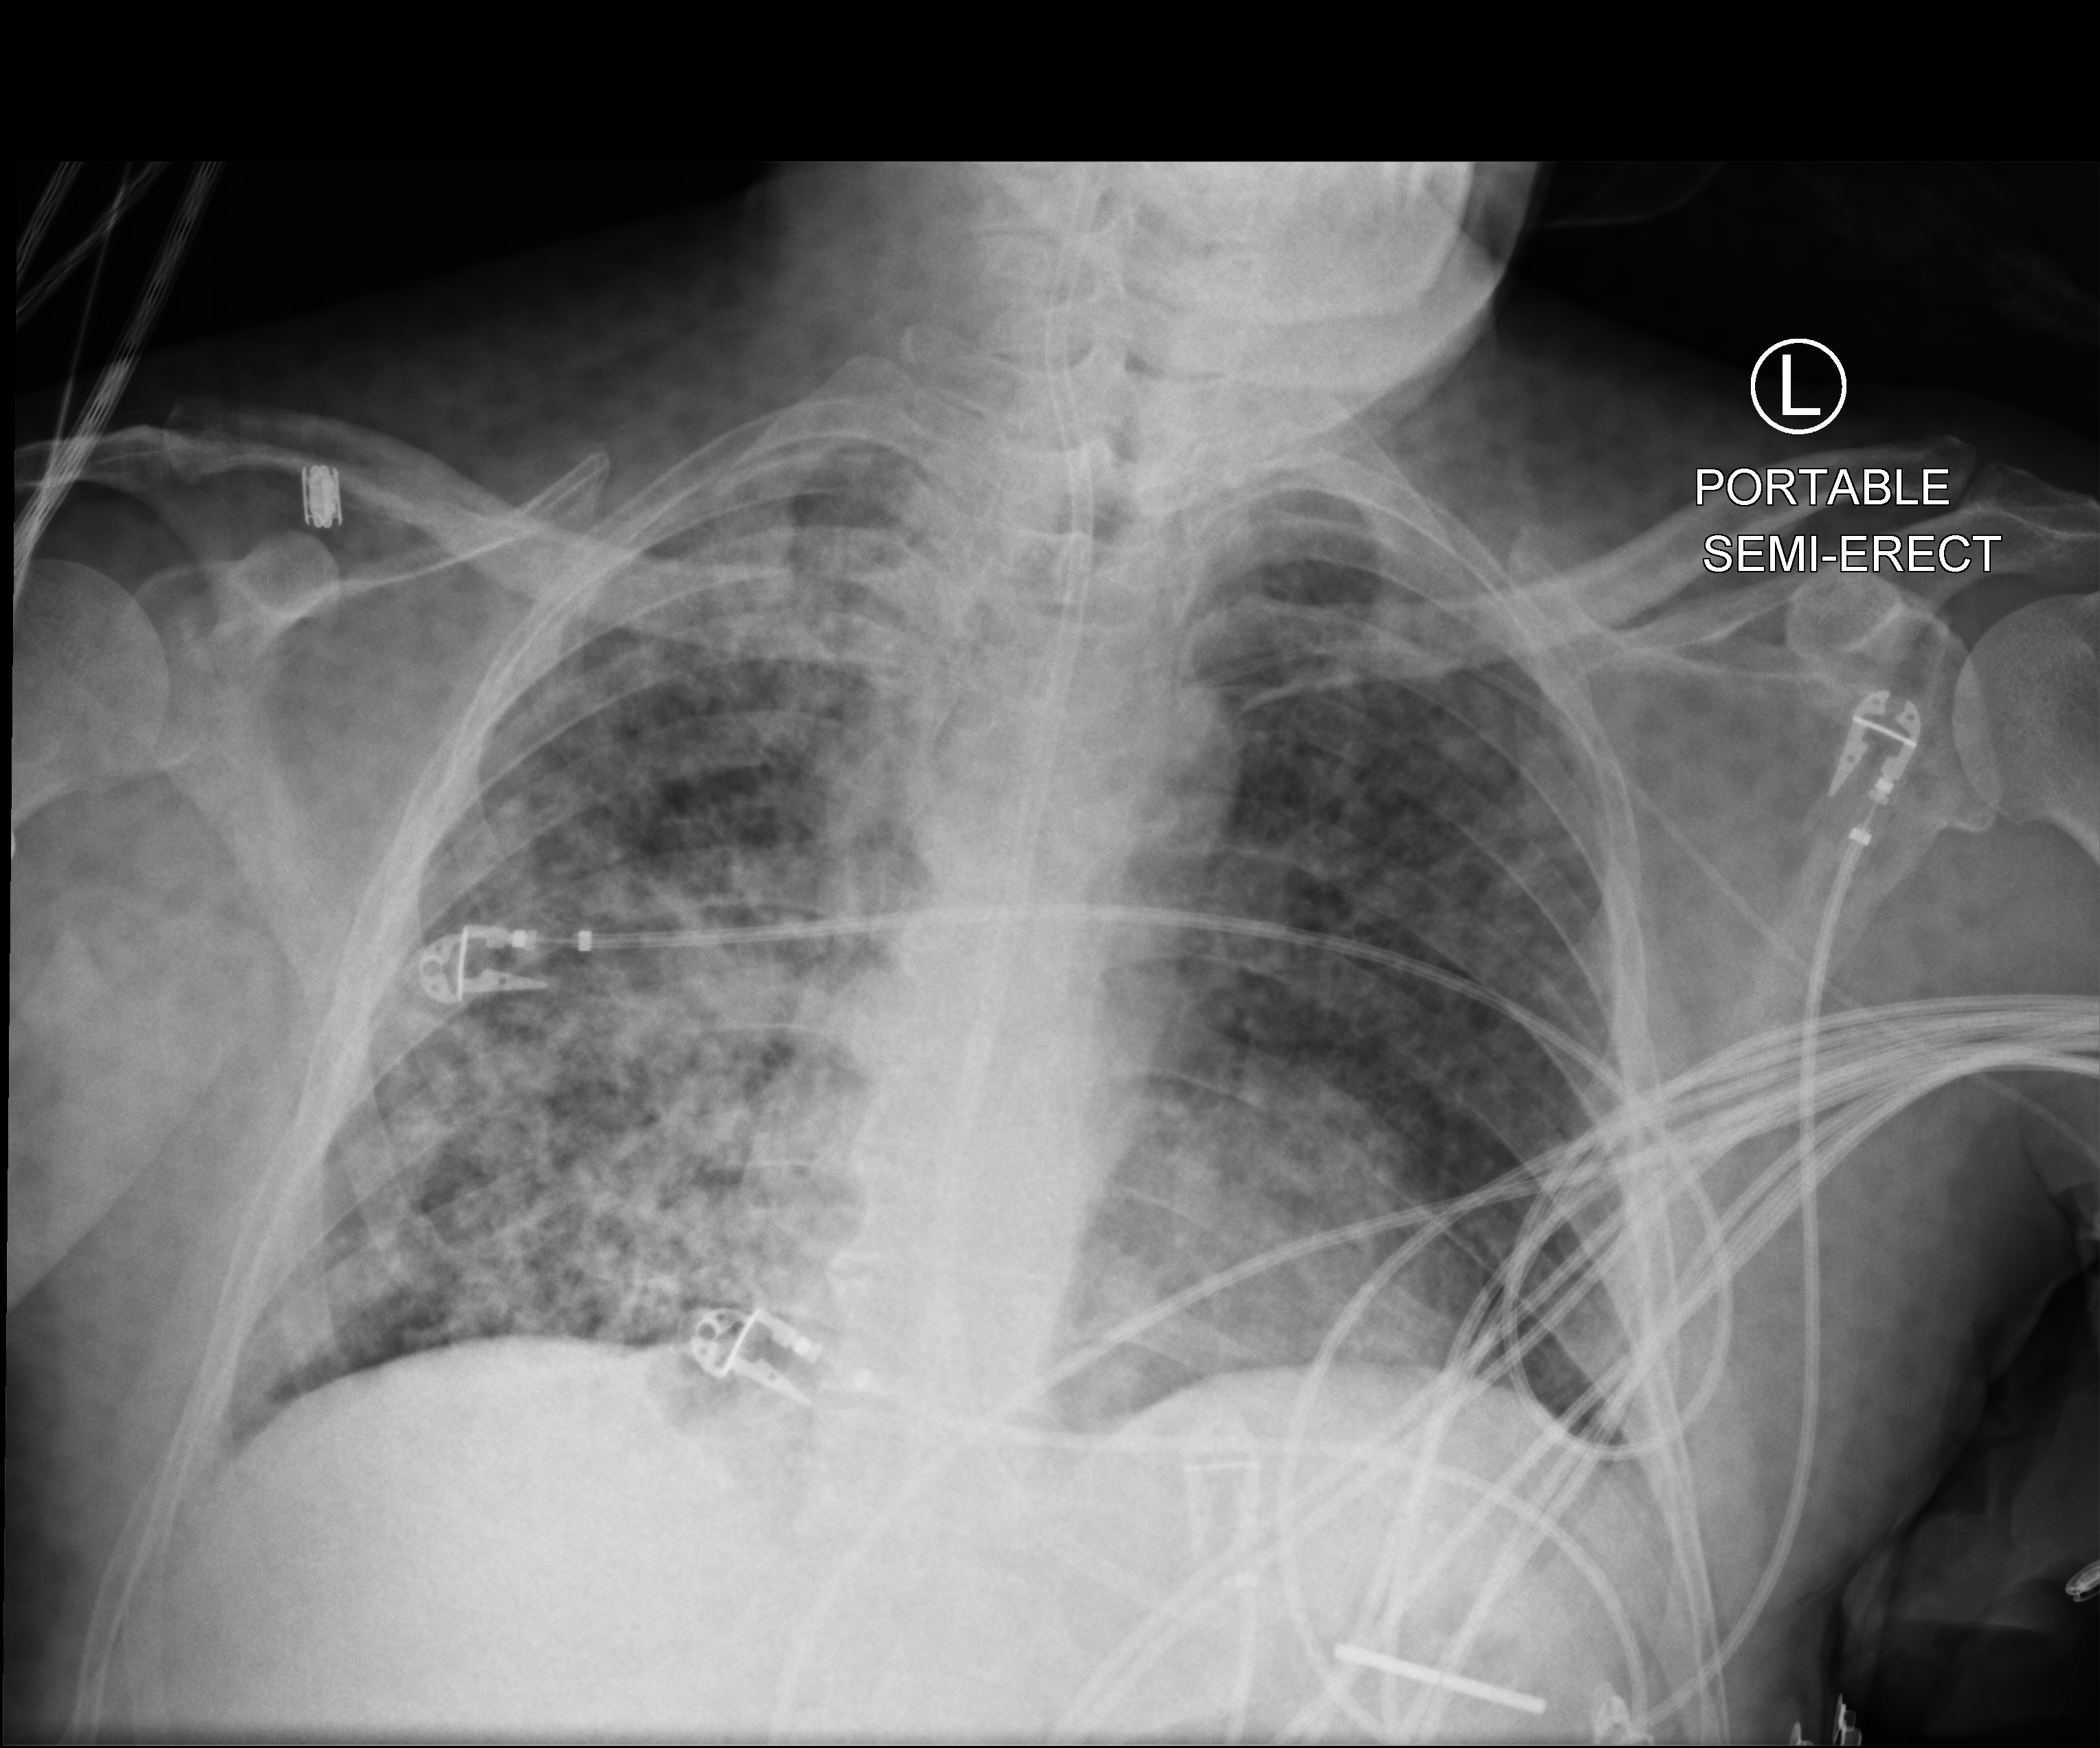
Chest X-ray (portable); anteroposterior (AP) projection. Patient hospitalised with COVID-19; male, aged 18–59 years.
From the hospital-stay record, not from the radiograph (when in the stay this image was taken is not recorded): chronic kidney disease (admission record): no; hypertension (admission record): yes; admitted to intensive care during this hospital stay: yes.